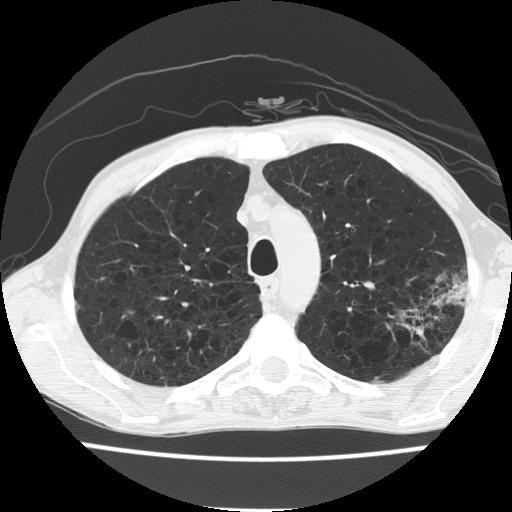
Low-dose screening chest CT, axial slice, baseline screening round, lung window (W 1500 / L -600 HU), 120 kVp. Male, age 60 years at enrolment. Current smoker at enrolment.
Expert-annotated lung lesion, bounding box (x1, y1, x2, y2) in pixels: (392, 261, 471, 343). Screening reader's record for this exam: no non-calcified nodule ≥4 mm recorded. Official screen result: negative screen, minor abnormalities not suspicious for lung cancer. Participant outcome: lung cancer diagnosed 490 days after this screen (after the second annual screen) — bronchiolo-alveolar carcinoma, mucinous, left upper lobe, stage IV (AJCC 6th edition).